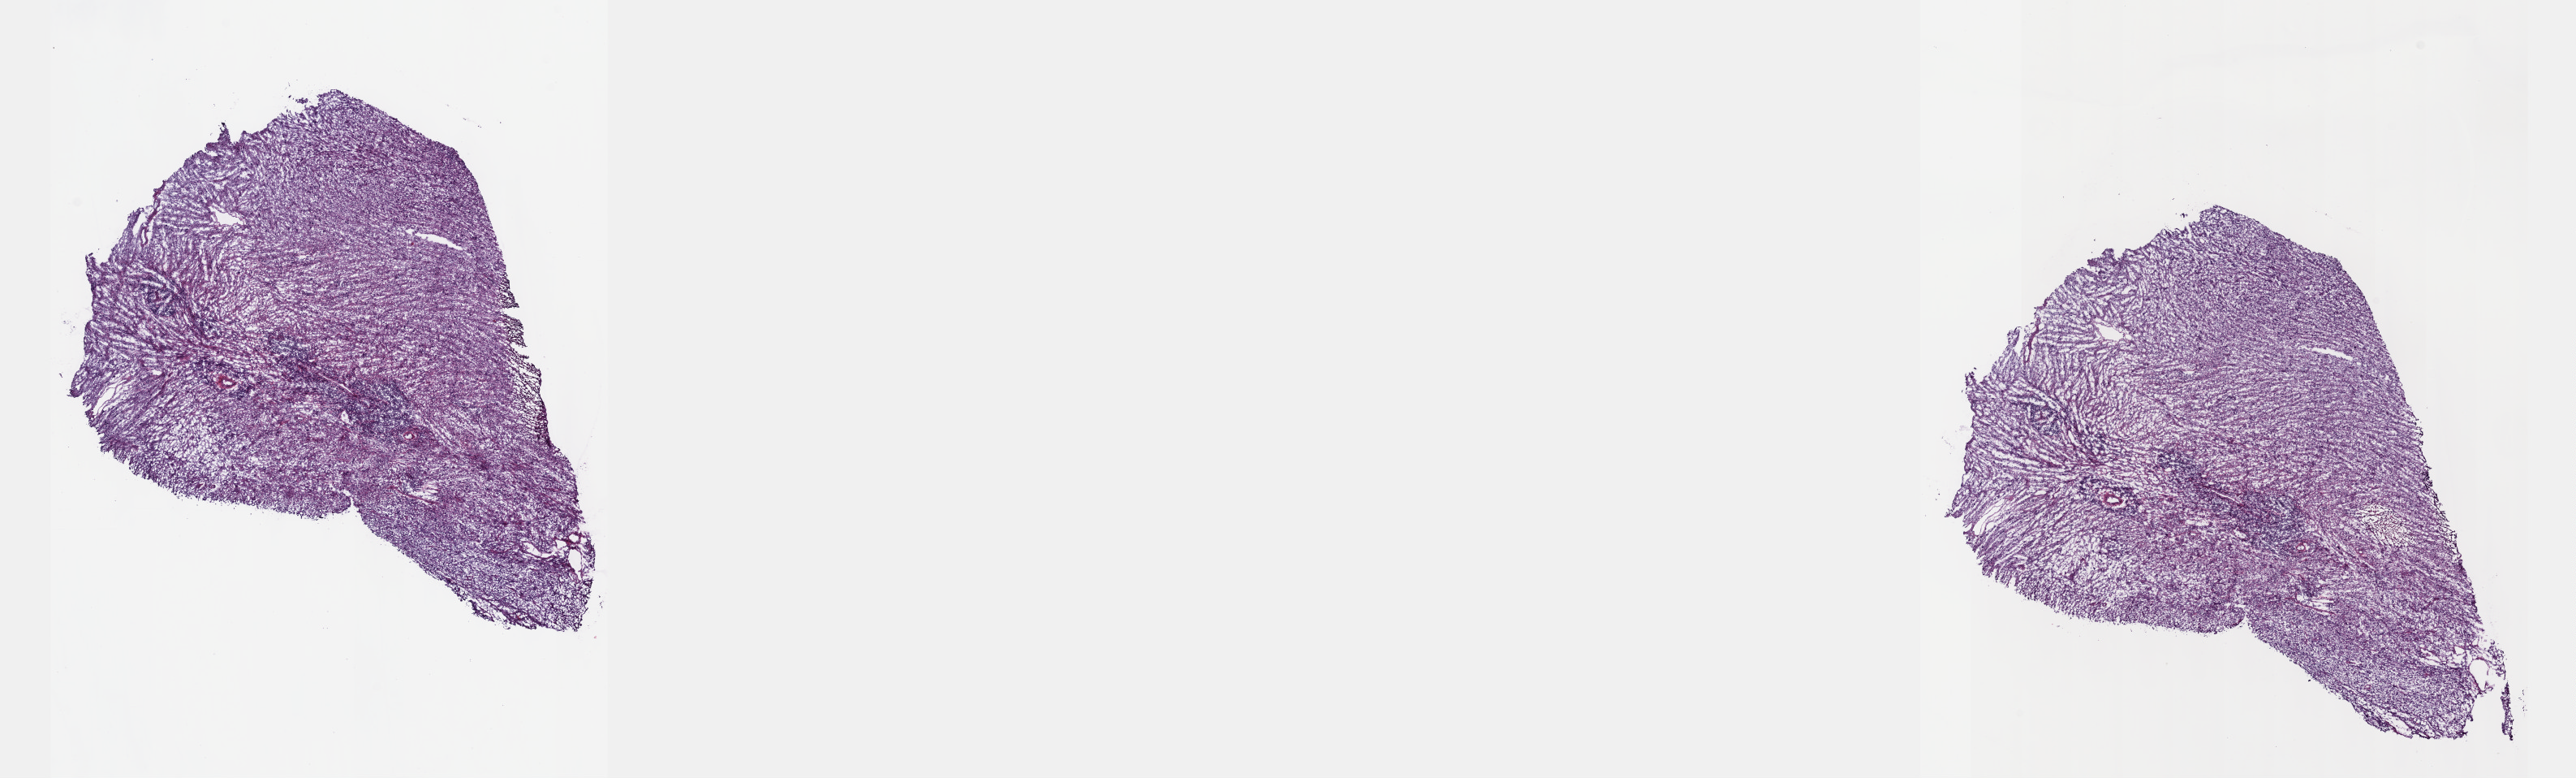
H&E whole-slide image — low-resolution overview of the scanned area, about 25.7 x 7.7 mm (acquisition: 40x scan). Frozen section from the top of the tissue portion. Sample: primary tumour, connective, subcutaneous and other soft tissues. Female patient; age at initial diagnosis 73 years. Composition of this section per pathologist review: tumour cells 100%, tumour nuclei 95%, normal cells 0%, stromal cells 0%, necrosis 0%. Inflammatory infiltration, as recorded: lymphocyte infiltration 0%, monocyte infiltration 0%, neutrophil infiltration 0%.
- diagnosis: Dedifferentiated liposarcoma (connective, subcutaneous and other soft tissues of lower limb and hip)